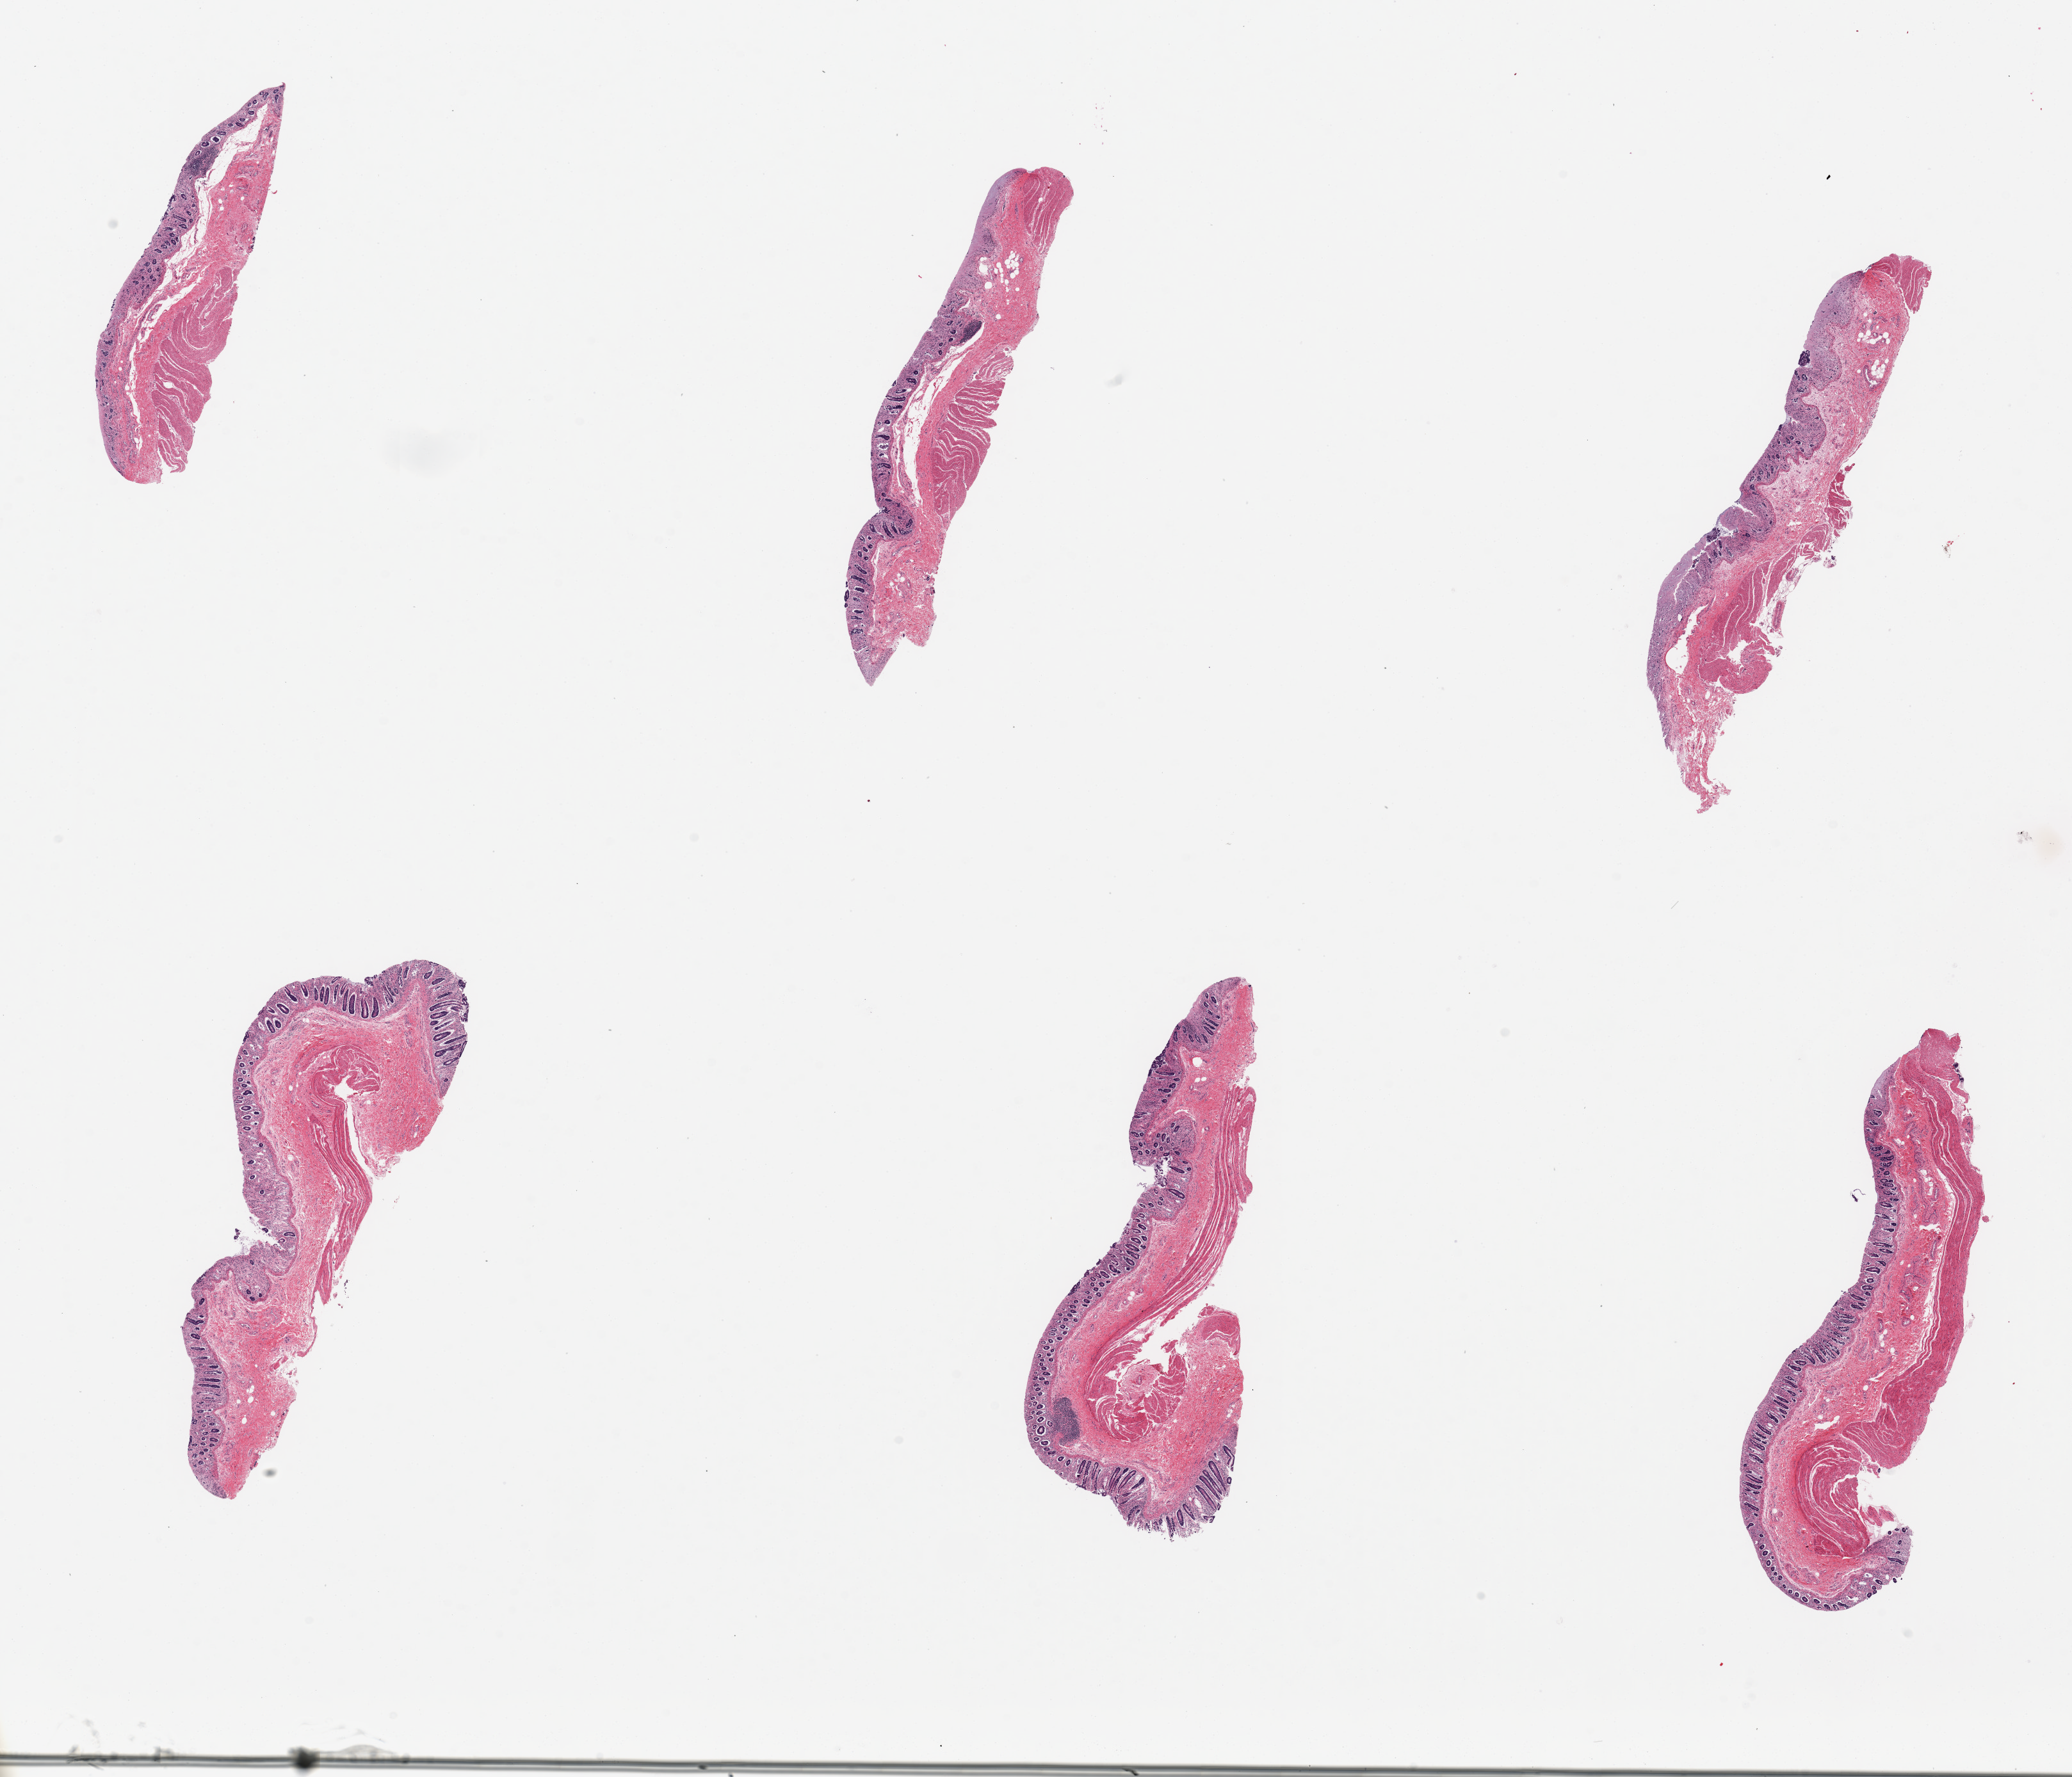
Digitized H&E-stained section, shown as a low-resolution overview of the whole scanned area (about 25.6 x 22.0 mm). PAXgene-fixed, paraffin-embedded tissue. Sampled site (target tissue): sigmoid colon. Tissue donor sample. Donor sex: male.
Pathologist's review note for this sample: 6 pieces, up to 7x2mm; all have mucosa and muscularis; mucosa largely autolyzed.